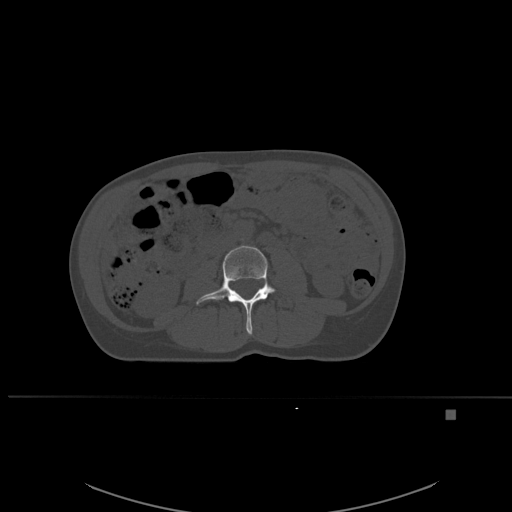
CT including the spine, one axial slice. Position 213 of 537 along the scan axis. Bone window (W 1800 / L 400 HU). 512 × 512 image matrix. Female patient, age 45 years. Case-level facts recorded for this patient, not image findings: primary cancer: lung.
Structures marked on this image (semi-automatically segmented with operator editing):
- L3 vertebra: bounding box (x1, y1, x2, y2) in pixels: (196, 245, 276, 335)